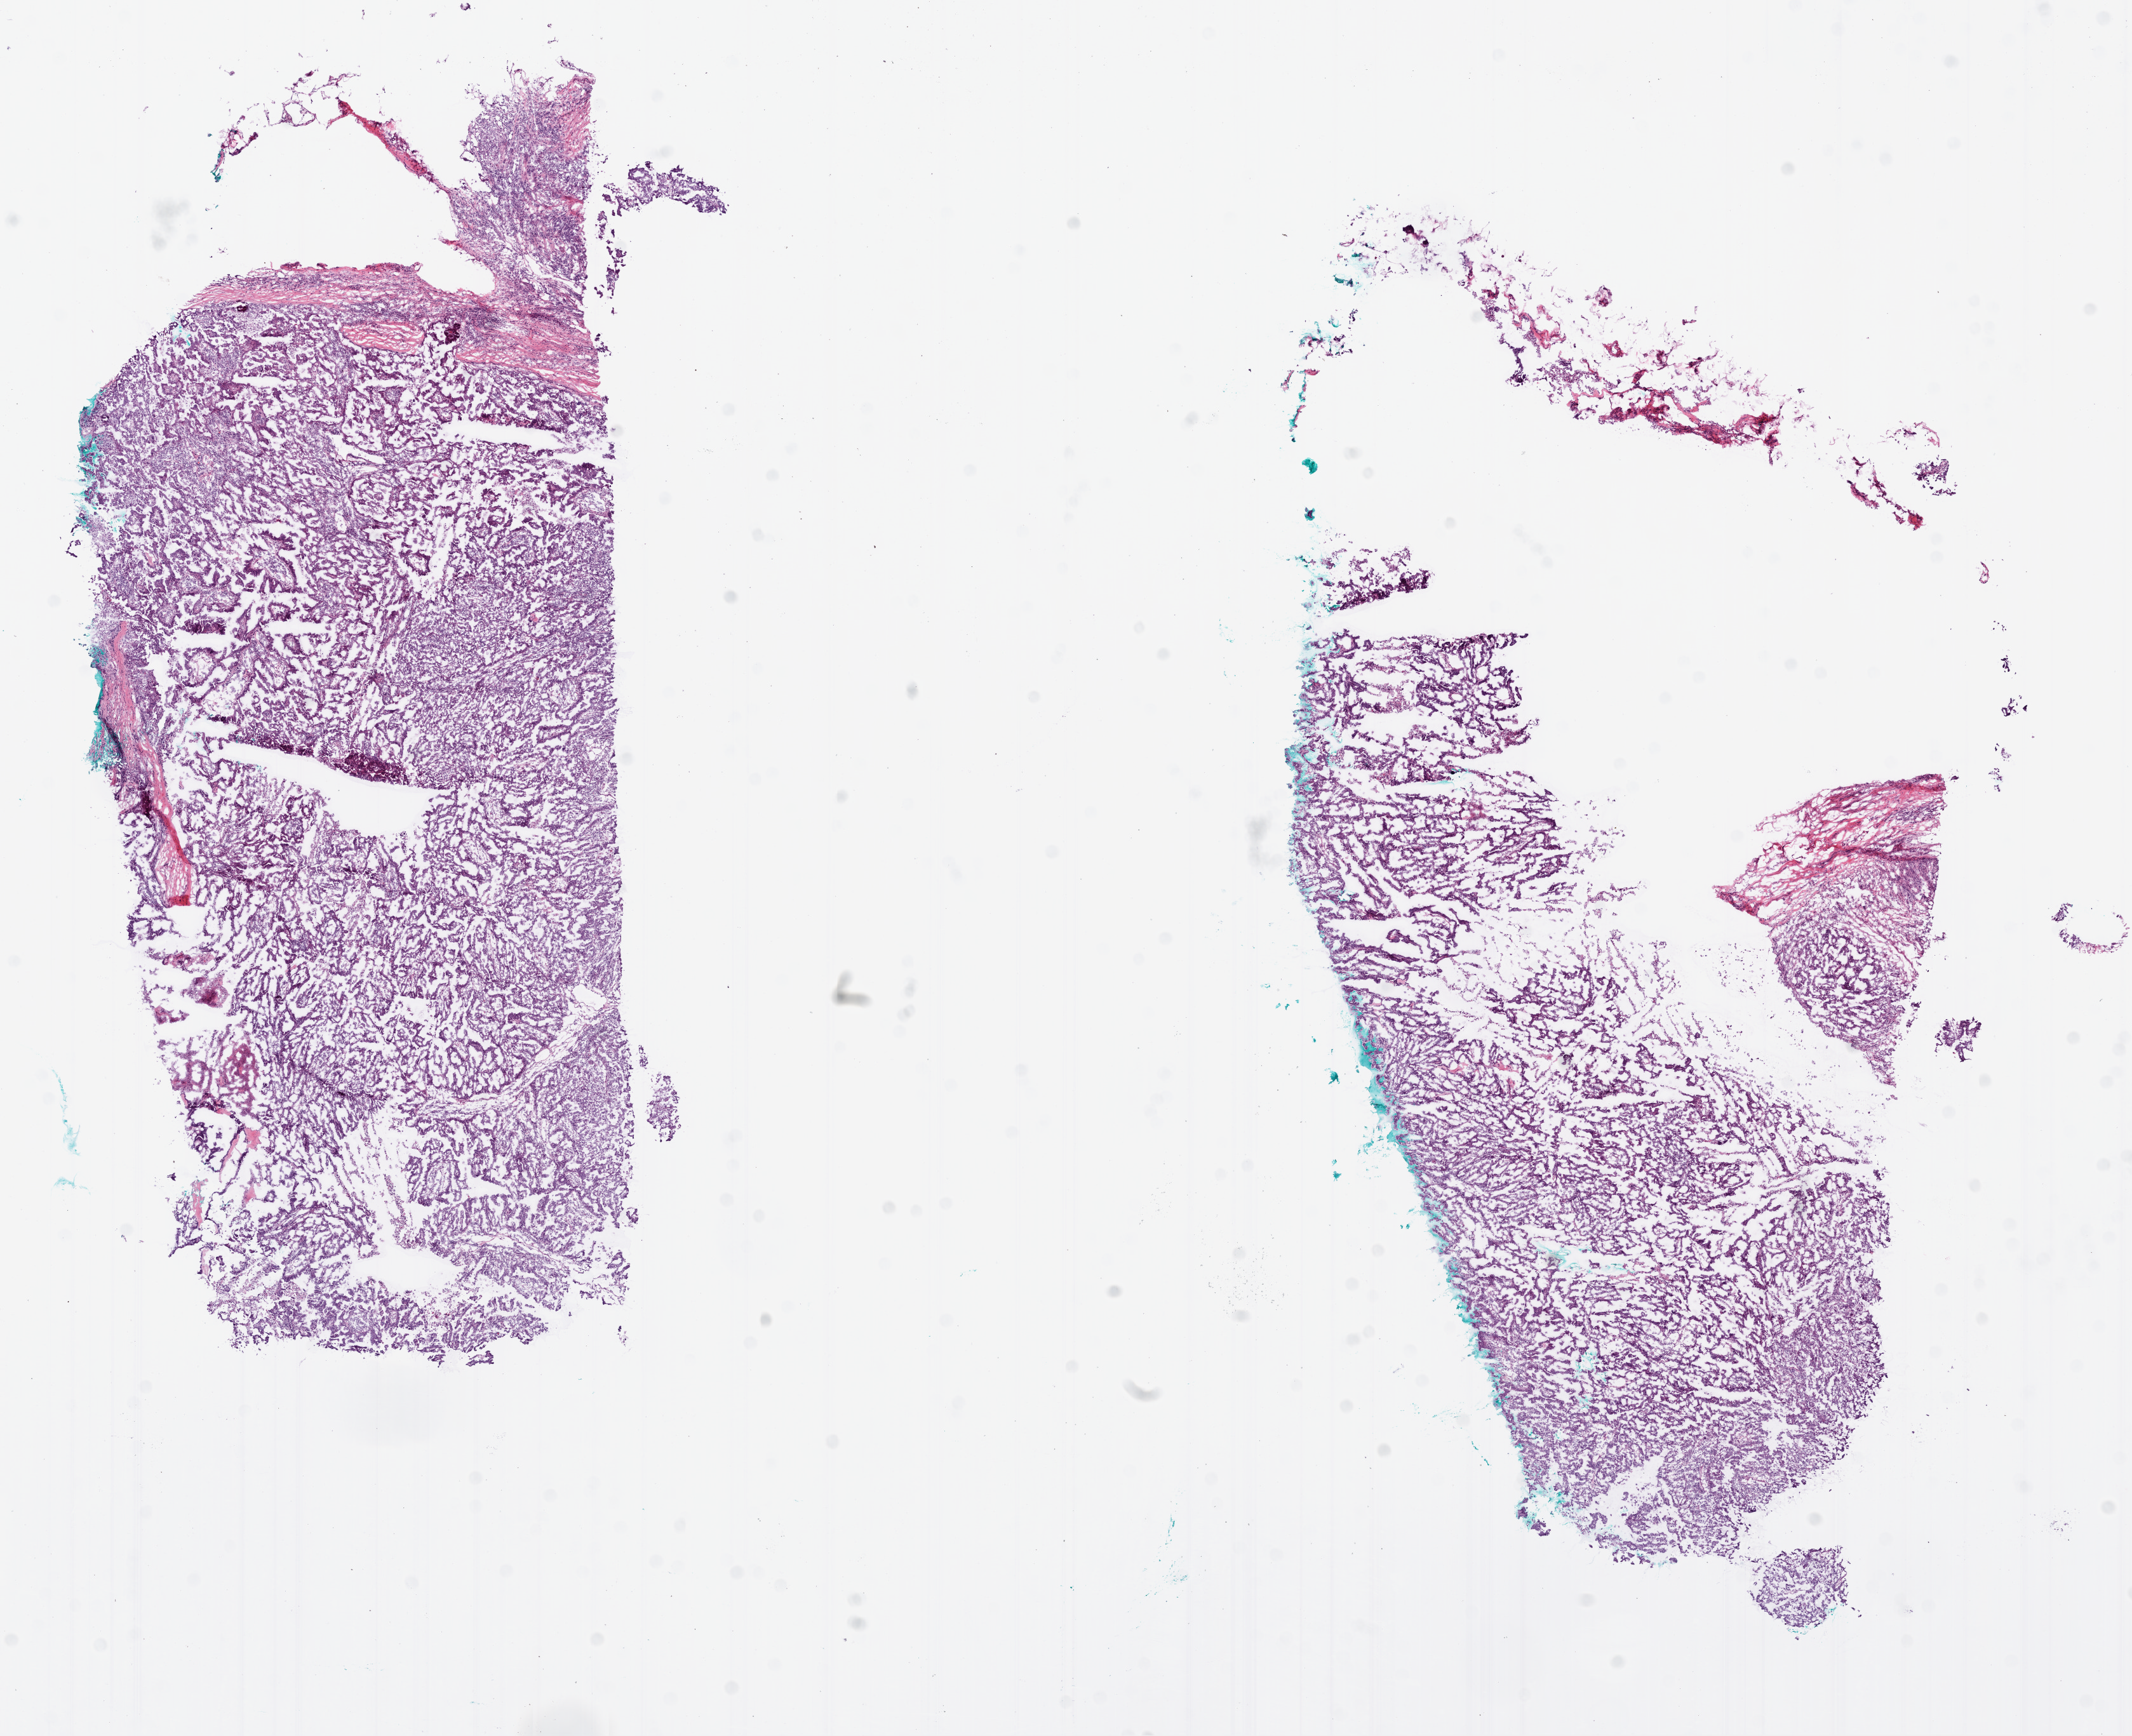
Digitized H&E tissue section (whole slide), shown as a low-resolution overview of the whole scanned area (about 13.5 x 11.0 mm), frozen section, sample: primary tumour, ovary. Female, age 63 years at initial diagnosis. Histologic grade: G3 (poorly differentiated). Pathologist review of this section (percent, as recorded): tumour cells 75%, tumour nuclei 80%, normal cells 10%, necrosis 5%.
• histologic diagnosis: Serous cystadenocarcinoma, NOS
• FIGO stage: IIIC